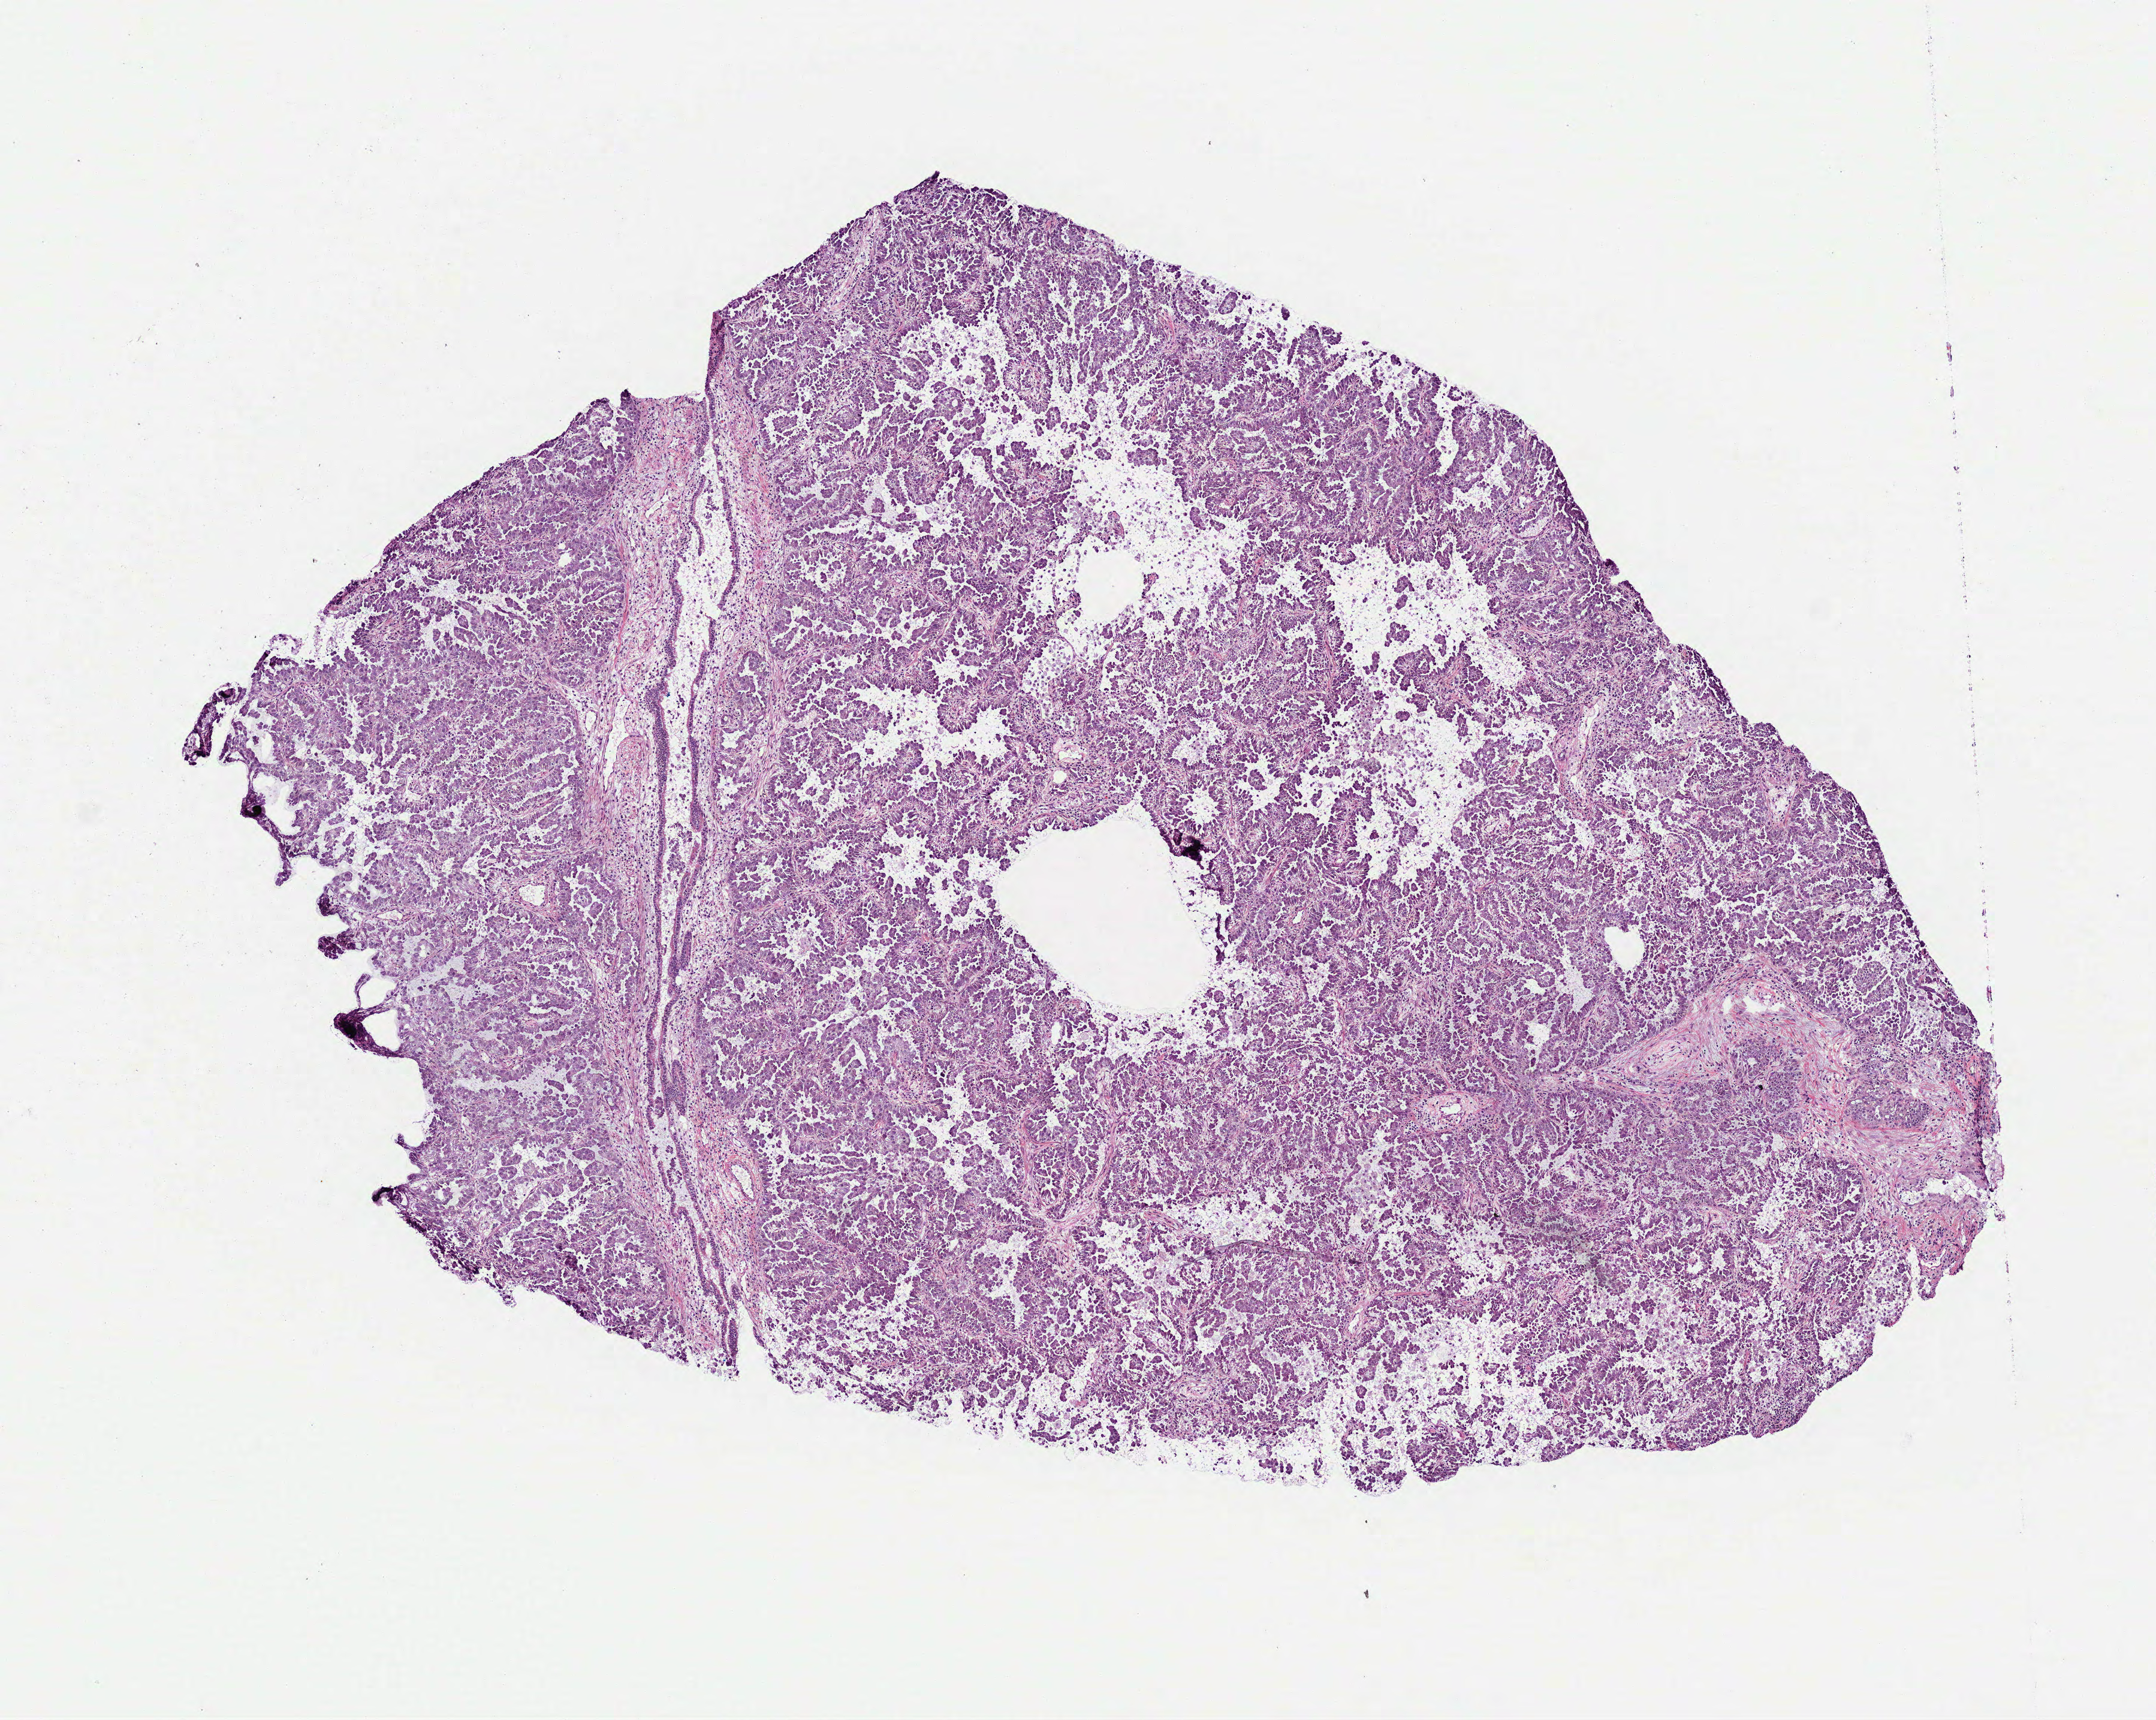
Whole-slide histology image, H&E-stained — whole scanned area (about 7.3 x 5.8 mm, acquisition: 40x scan) shown as a low-resolution overview; frozen section from the bottom of the tissue portion; lung, primary tumour sample. Female patient; age at initial diagnosis 52 years. Slide review estimates, as recorded: tumour cells 85%, tumour nuclei 80%, normal cells 0%, stromal cells 15%, necrosis 0%.
• diagnosis: Adenocarcinoma, NOS (lower lobe, lung)
• AJCC pathologic stage: IB (7th edition)